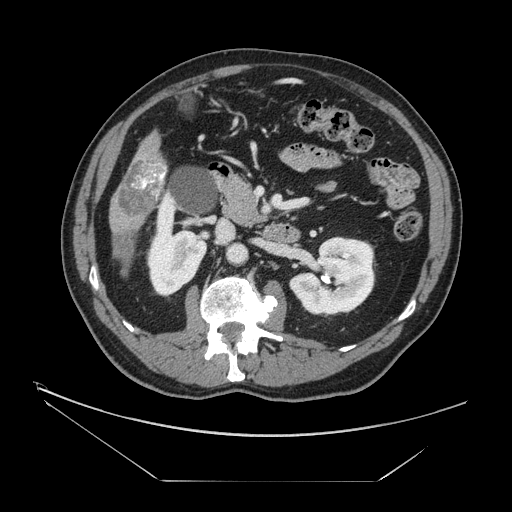
Contrast-enhanced abdominal CT, one axial slice. Slice 58 of 161 in the series (ordered by position). Reconstruction kernel STANDARD. 120 kVp. Soft-tissue window (W 400 / L 40 HU). 2.5 mm slice thickness. 512 × 512 image matrix, field of view 440 × 440 mm. Male patient, age 65 years. From the clinical record (not read from this slice): diagnosis: colorectal cancer liver metastases, imaged before liver resection; multiple liver metastases: yes; largest metastasis: 4.2 cm.
Outlined on this slice (manually delineated by an expert):
- liver: bounding box (x1, y1, x2, y2) in pixels: (110, 134, 166, 259)
- portal vein (with intrahepatic branches): (136, 170, 164, 193)
- liver metastasis: (114, 231, 134, 267)
- liver metastasis: (118, 156, 167, 217)